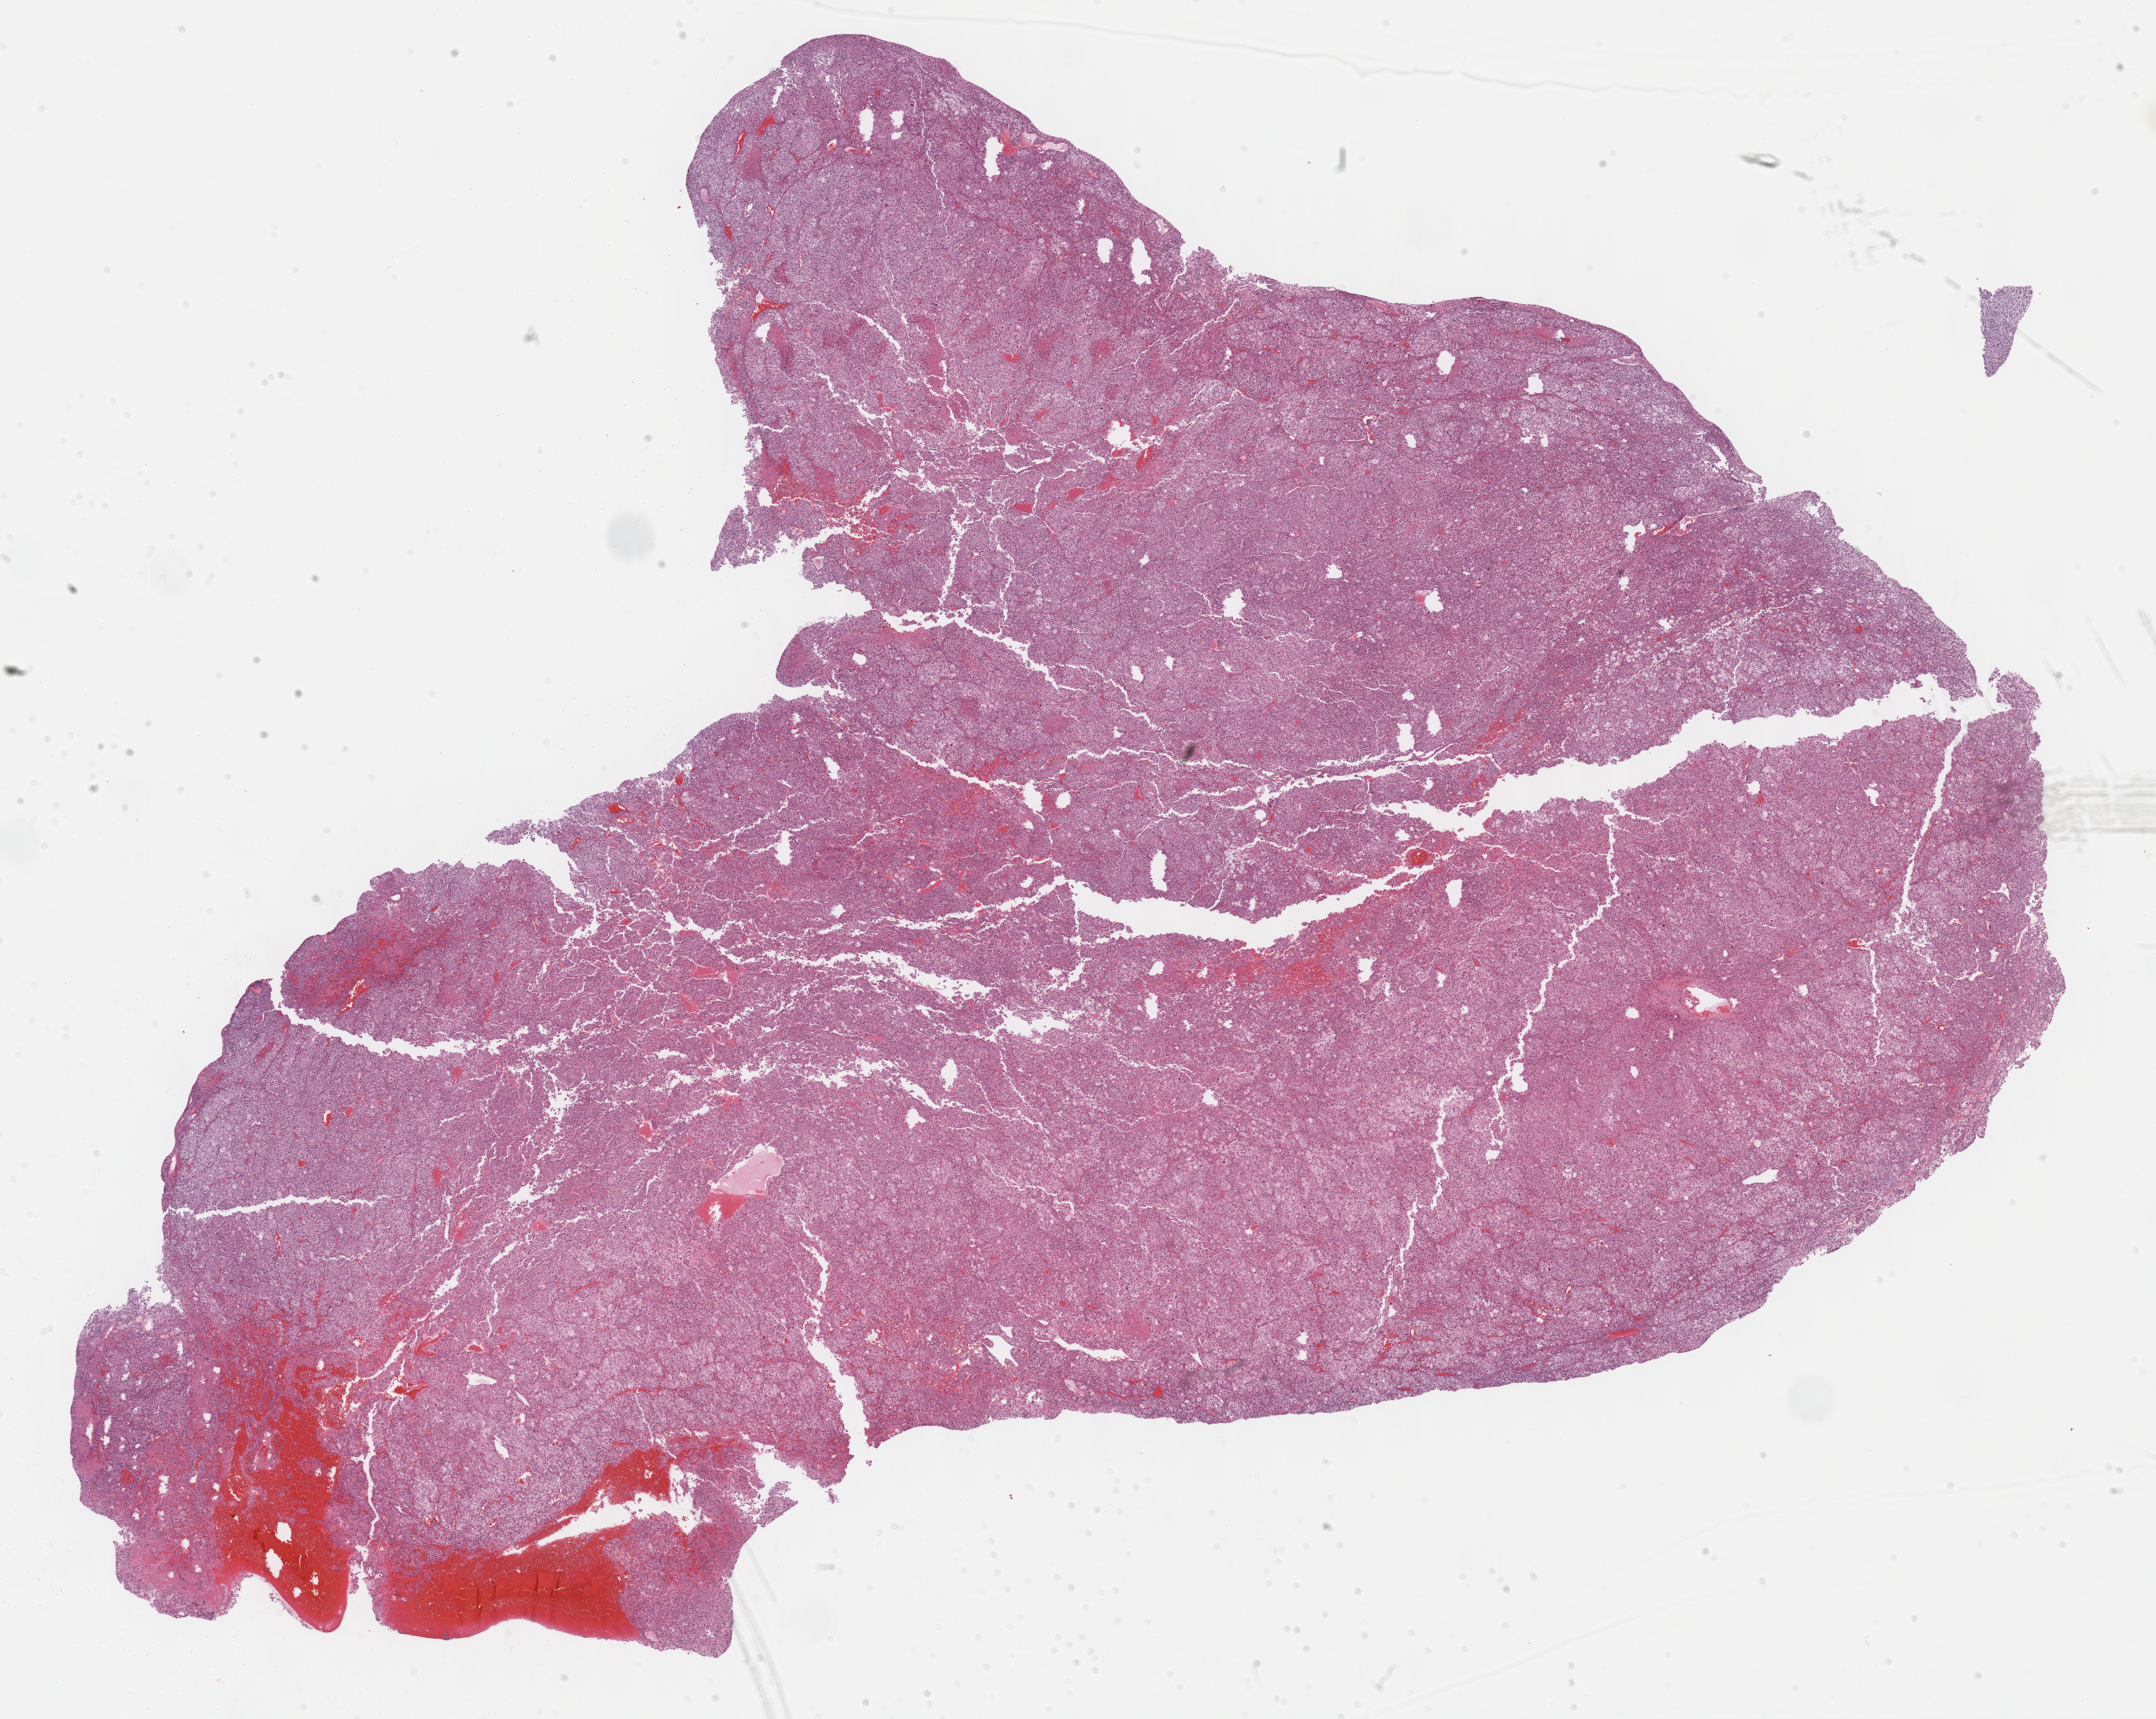
Whole-slide histology image, H&E-stained — whole scanned area (about 22.1 x 17.7 mm) shown as a low-resolution overview, formalin-fixed paraffin-embedded (FFPE) diagnostic section, primary tumour sample from the adrenal cortex. Female, age 68 years at initial diagnosis.
Lymph nodes positive (case pathology): 1 of 2 examined. Pathologic diagnosis: Adrenal cortical carcinoma (cortex of adrenal gland).